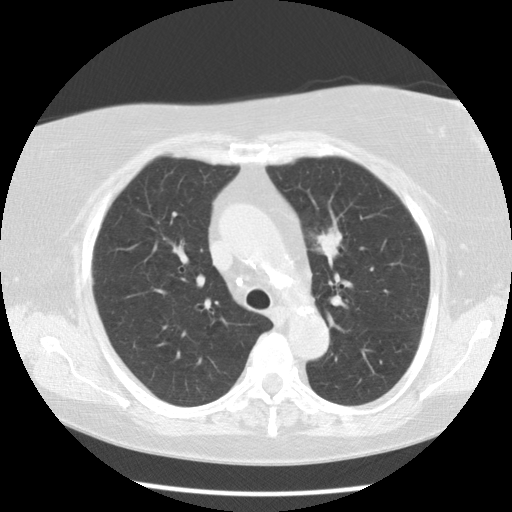
Low-dose screening chest CT, one axial slice. Slice 81 of 109 in the series (ordered by position). Reconstruction kernel STANDARD. 120 kVp. Lung window (W 1500 / L -600 HU). 512 × 512 image matrix.
Outlined on this slice (manually delineated by an expert):
- lesion 1 (tumor, upper lobe of left lung): bounding box <316,227,342,263> (left, top, right, bottom; pixels)